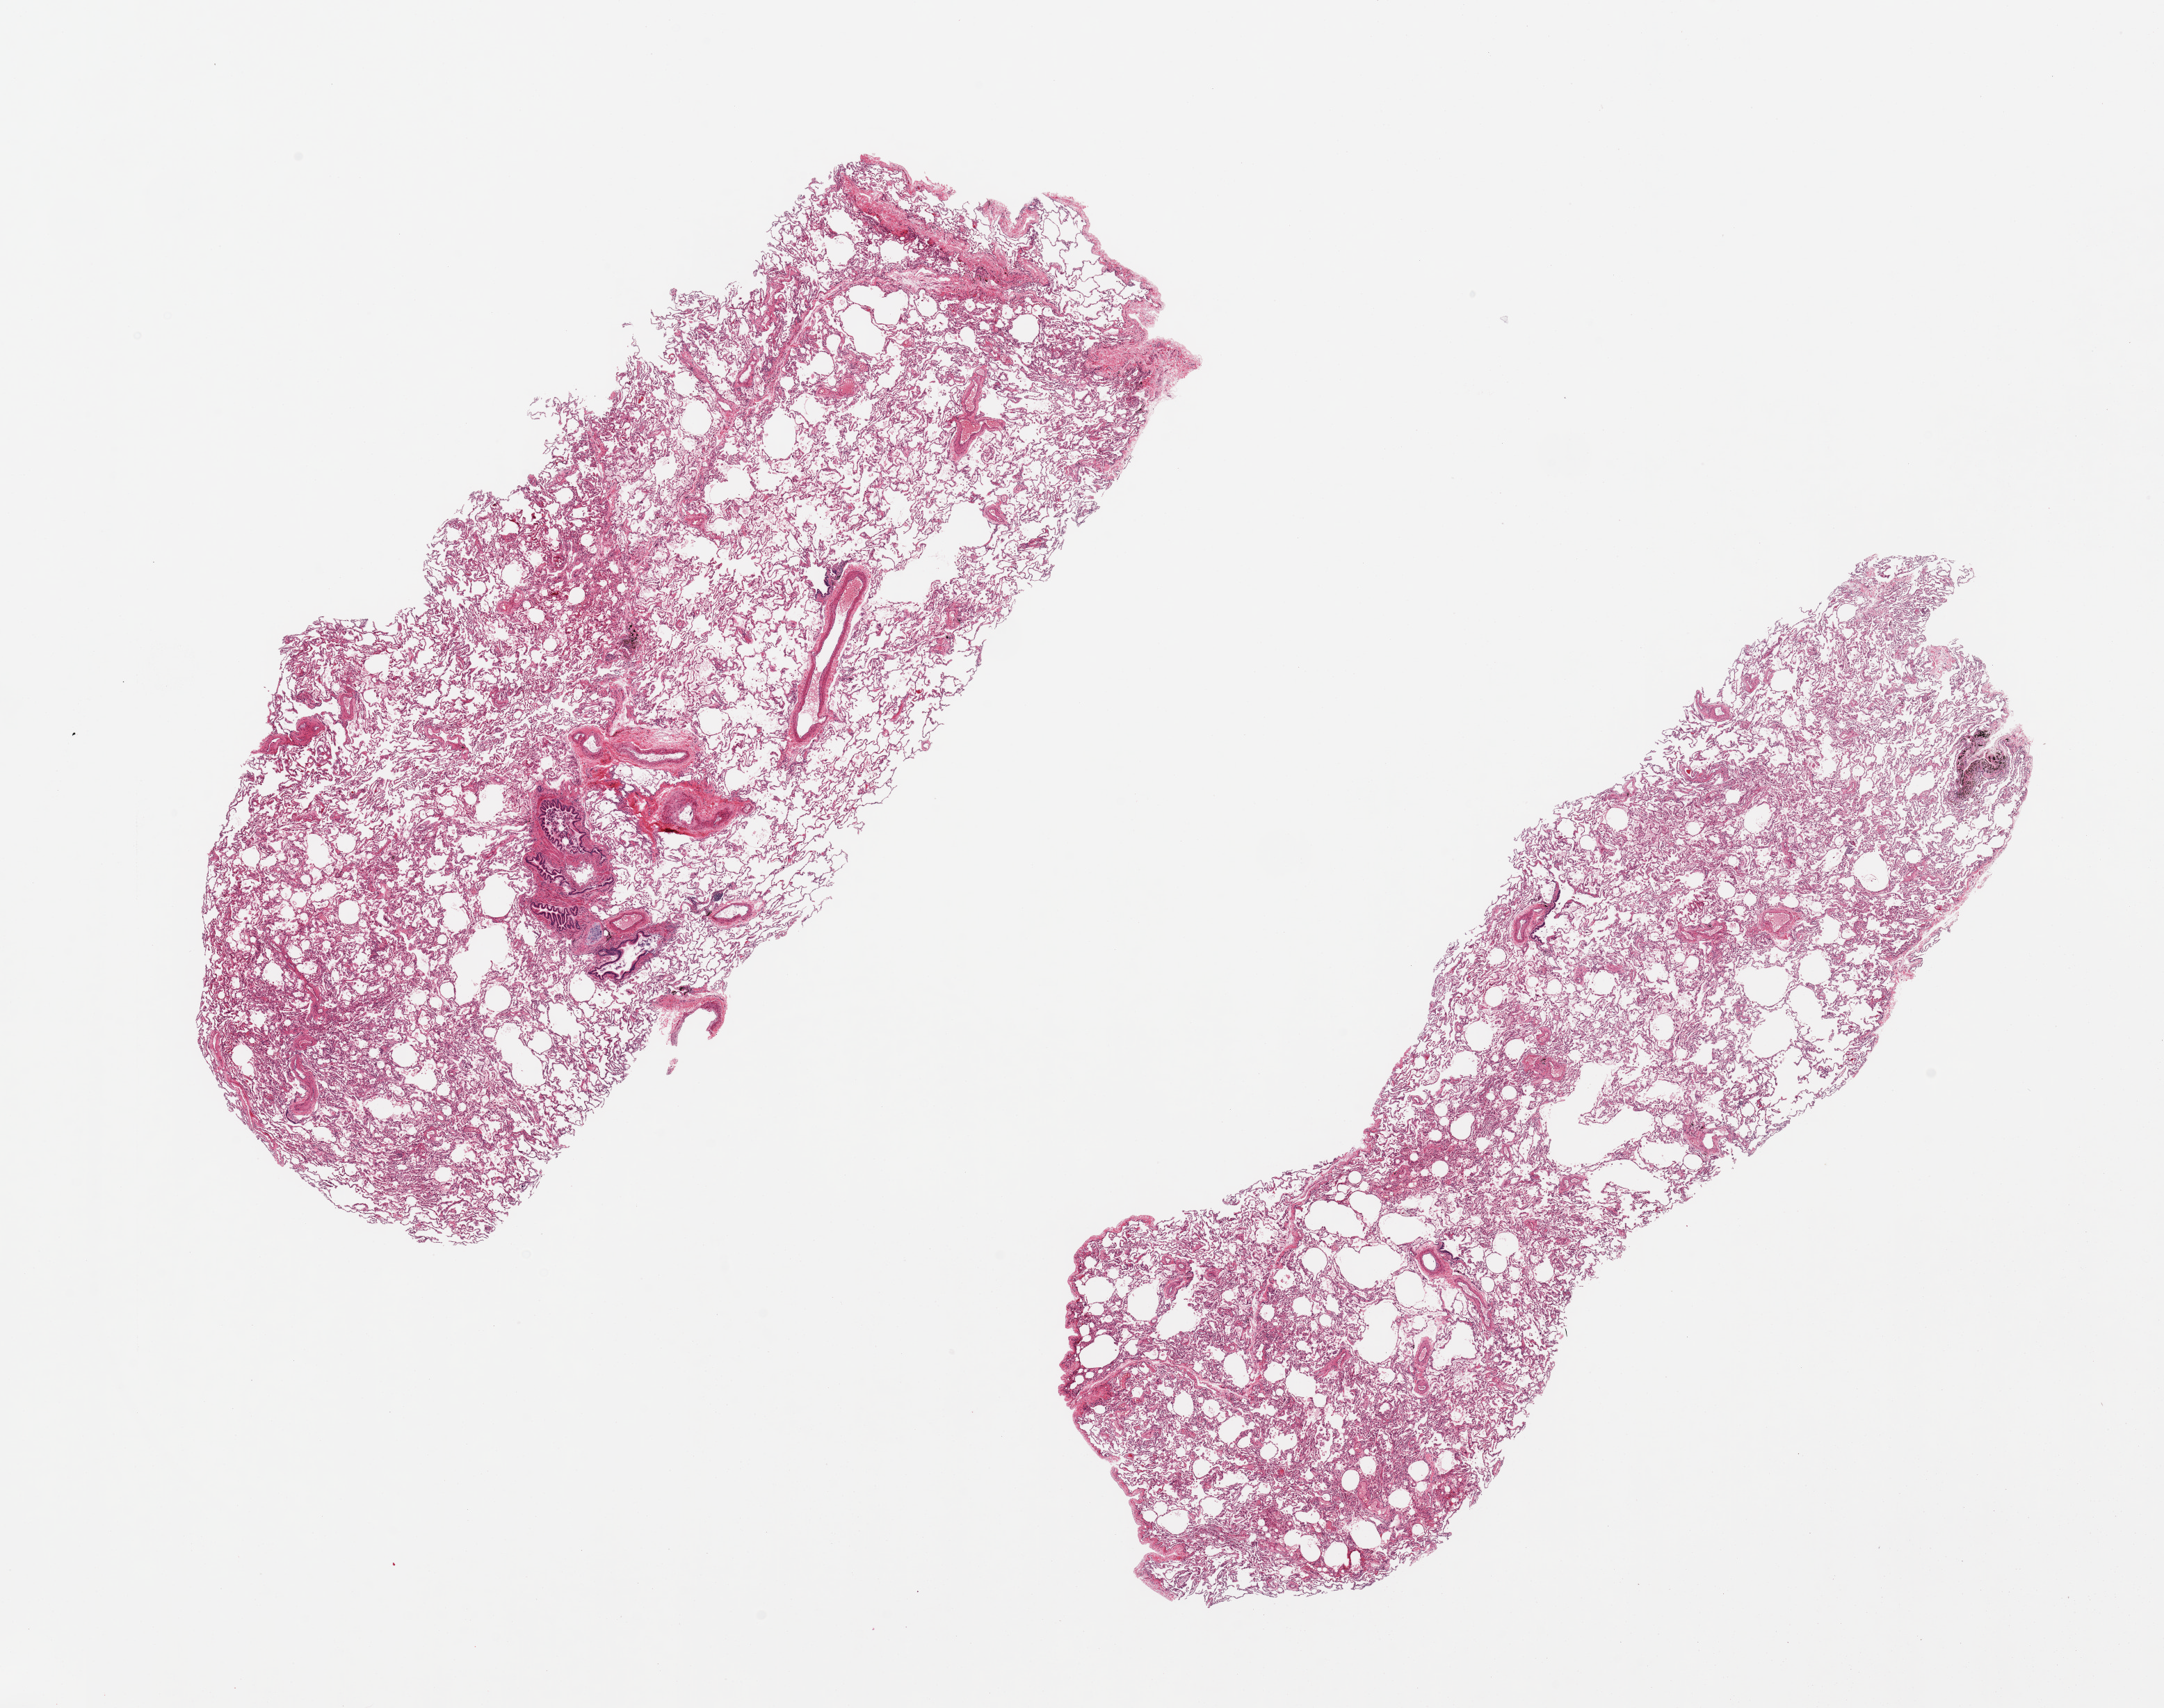
Digitized hematoxylin and eosin (H&E)-stained section, brightfield — low-resolution overview of the scanned area, about 24.6 x 19.4 mm (from a 20x scan). PAXgene-fixed, paraffin-embedded tissue. Section of lung (target tissue). Donor tissue sample. Donor sex: male.
Review note (as recorded): 2 pieces, numerous hemosiderin-laden macrophages, some emphysematous change.